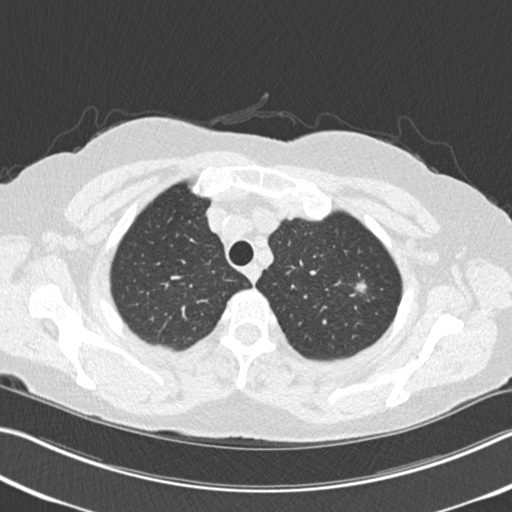
Low-dose screening chest CT, one axial slice. Slice 190 of 225 in the series (ordered by position). 120 kVp. Lung window (W 1500 / L -600 HU). 2 mm slice thickness. 512 × 512 image matrix, field of view 342 × 342 mm.
Structures marked on this image (expert manual segmentation):
- lesion 1 (tumor): bounding box (x1, y1, x2, y2) in pixels: (355, 282, 366, 293)